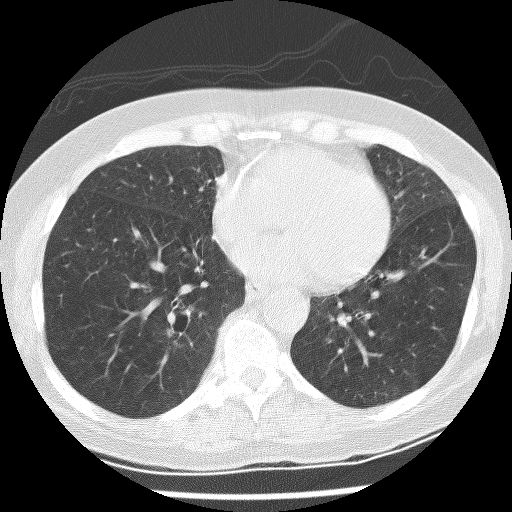
Low-dose screening chest CT, one axial slice; reconstruction kernel BONE; 120 kVp; lung window (W 1500 / L -600 HU); 512 × 512 image matrix, field of view 300 × 300 mm.
Annotated regions visible in this slice (expert manual segmentation):
- lesion 1 (tumor, lower lobe of right lung): bounding box <166,326,180,337> (left, top, right, bottom; pixels)